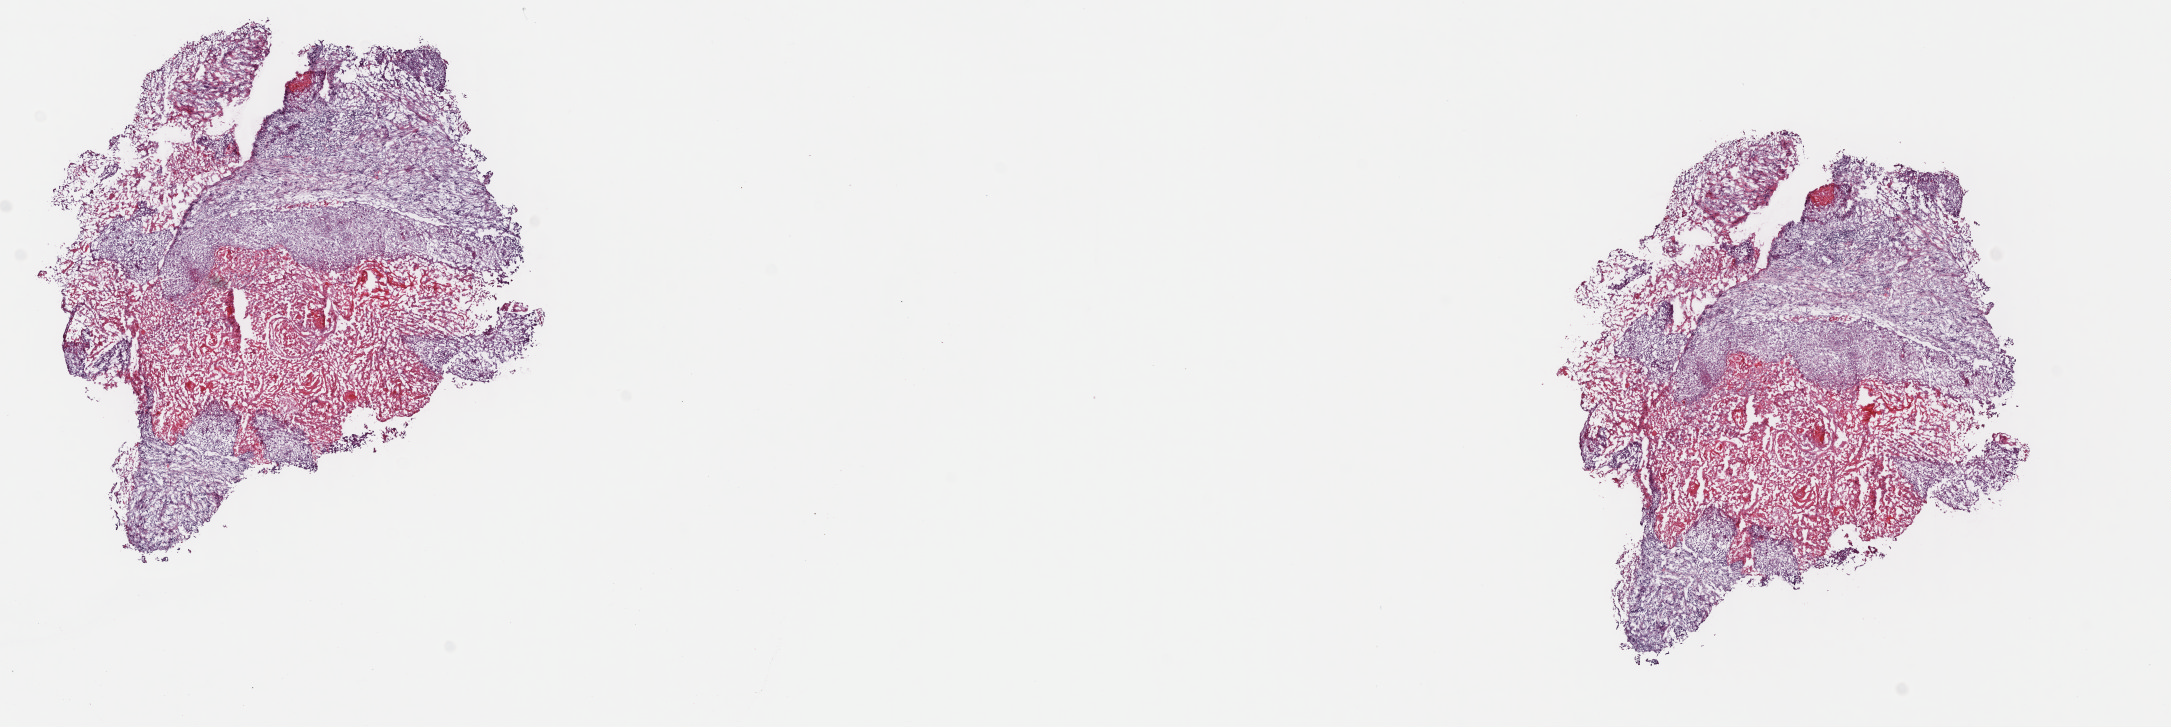
H&E whole-slide image, low-resolution overview of the scanned area, about 17.1 x 5.7 mm (slide scanned at 40x); frozen section; primary tumour sample from the head and neck. Male, age 59 years at initial diagnosis. Histologic grade: G2 (moderately differentiated). Composition of this section per pathologist review: tumour cells 60%, tumour nuclei 60%, normal cells 0%, stromal cells 40%, necrosis 0%. Inflammatory infiltration, as recorded: lymphocyte infiltration 40%, monocyte infiltration 20%, neutrophil infiltration 20%.
• pathologic diagnosis: Squamous cell carcinoma, NOS (cheek mucosa)
• AJCC pathologic stage: IVA
• lymph nodes positive (case pathology): 0 of 45 examined